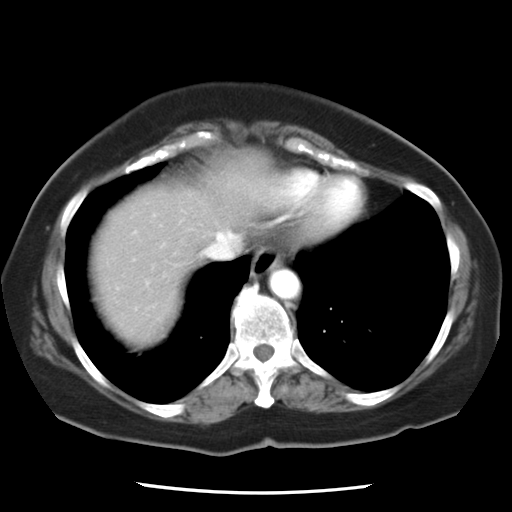
Contrast-enhanced abdominal CT, one axial slice. Slice 22 of 24 in the series (ordered by position). Reconstruction kernel STANDARD. Intravenous contrast given. Soft-tissue window (W 400 / L 40 HU). 7.5 mm slice thickness. 512 × 512 image matrix, field of view 312 × 312 mm. Female patient, age 71 years. Case-level facts recorded for this patient, not image findings: diagnosis: colorectal cancer liver metastases, imaged before liver resection; multiple liver metastases: no; largest metastasis: 4.3 cm; chemotherapy before resection: no.
Annotated regions visible in this slice (expert manual segmentation):
- hepatic veins: box from (x=204, y=231) to (x=236, y=259) px
- liver: (x=89, y=154)–(x=282, y=341)
- planned liver remnant (the part of the liver to remain after resection): (x=89, y=180)–(x=234, y=341)